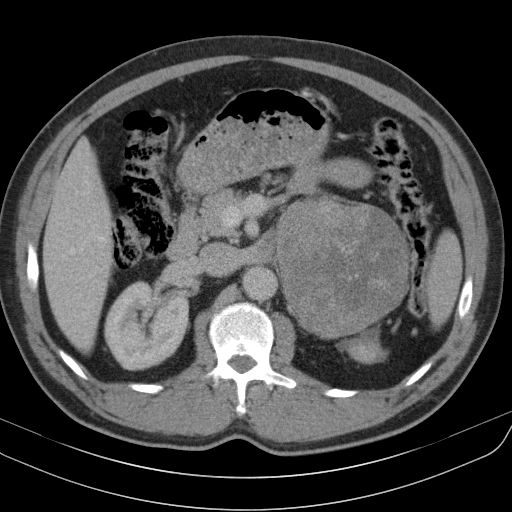
Contrast-enhanced abdominal CT, one axial slice. Position 64 of 91 along the scan axis. Reconstruction kernel B31s. 130 kVp. Intravenous contrast given. Soft-tissue window (W 400 / L 40 HU). 5 mm slice thickness. 512 × 512 image matrix. Male patient, age 51 years. Case-level facts recorded for this patient, not image findings: diagnosis: adrenocortical carcinoma; tumour side: left adrenal; tumour size at pathology: 18 cm; Ki-67 index: 40 %; stage (as recorded): 3.
Annotated regions visible in this slice (semi-automatically segmented with operator editing):
- mass: bounding box <280,202,408,336> (left, top, right, bottom; pixels)